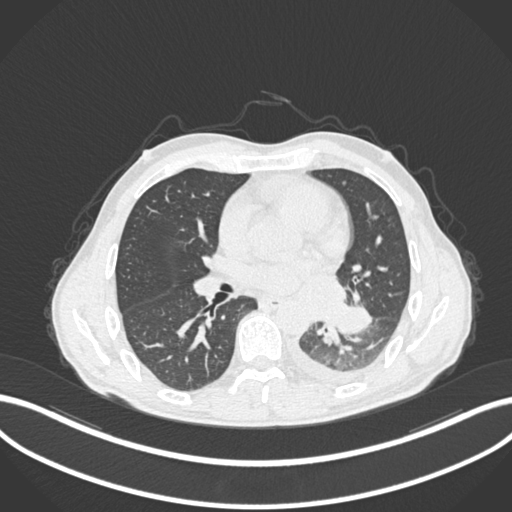
Chest CT, one axial slice. Position 119 of 222 along the scan axis. Reconstruction kernel B30f. 120 kVp. Lung window (W 1500 / L -600 HU). 1 mm slice thickness. 512 × 512 image matrix, field of view 400 × 400 mm. Patient: male, 47 years. From the clinical record (not read from this slice): clinical TNM (as recorded): T3 N1 M1c; histopathological grade: G3.
Outlined on this slice (rectangle marked by the reading radiologist):
- lung tumour (recorded histology: small cell carcinoma): bounding box [x1, y1, x2, y2] px = [330, 301, 376, 336]